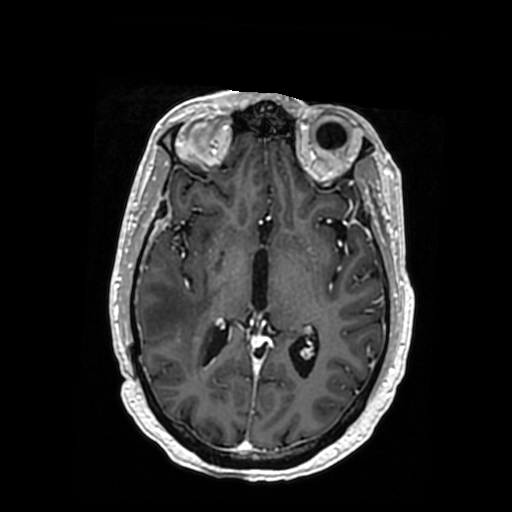
Brain MRI from a brain-tumour surgery series, one axial slice. T1-weighted post-contrast. 0.5 mm slice thickness. 512 × 512 image matrix, field of view 260 × 260 mm. Case-level facts recorded for this patient, not image findings: histopathology: Oligodendroglioma; WHO grade: 3.
Outlined on this slice (outlined manually by an expert reader):
- tumour: bounding box [x1, y1, x2, y2] px = [151, 337, 208, 347]